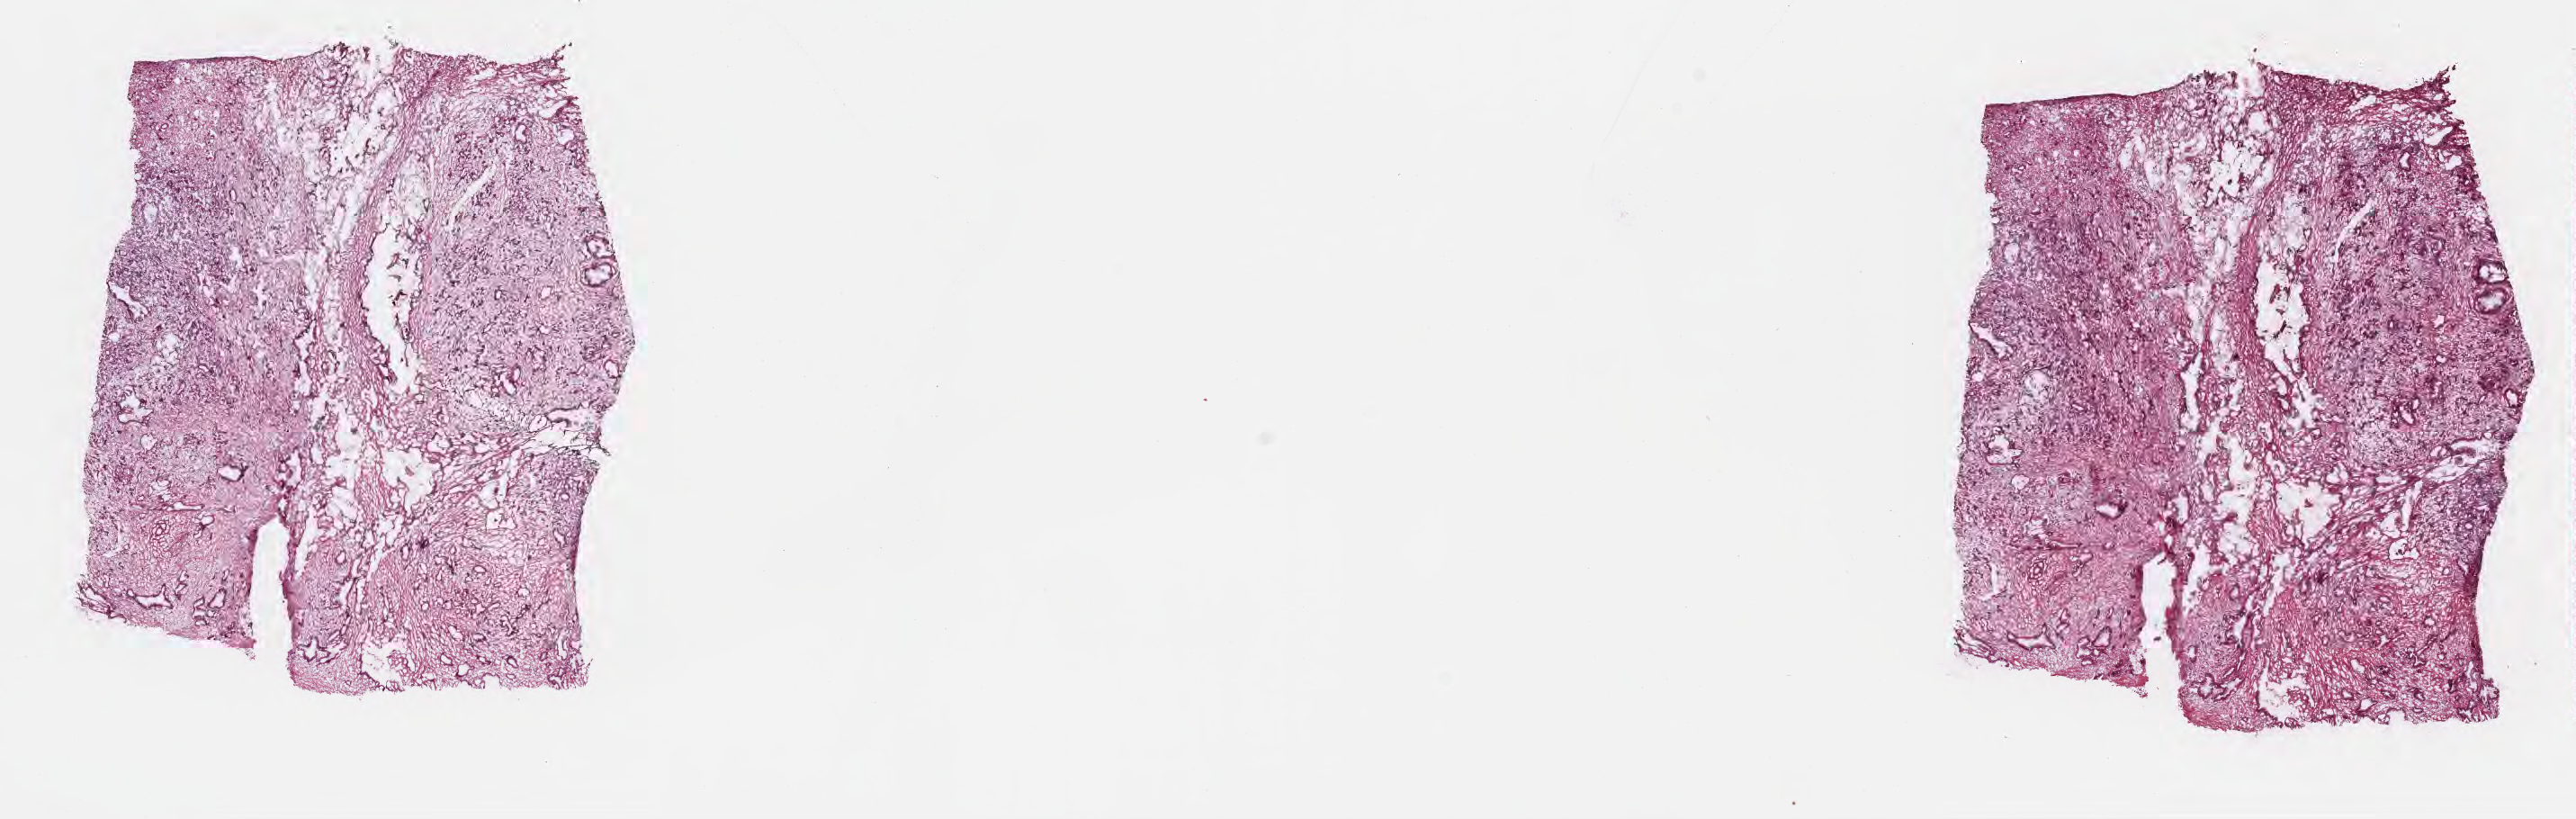
Whole-slide image, hematoxylin and eosin (H&E) stain — a low-resolution overview of the entire scanned area, about 23.2 x 7.4 mm; cryosection; primary tumor; anatomic site: head of pancreas. Male patient; age at initial diagnosis 63 years. Tumor grade: G2 (moderately differentiated). Pathologist review of this section (percent, as recorded): tumor cells 20%, tumor nuclei 40%, stromal cells 60%, necrosis 0%, normal cells 20%. Inflammatory infiltration, as recorded: lymphocyte infiltration 0%, monocyte infiltration 0%, neutrophil infiltration 0%.
Diagnosis: Infiltrating duct carcinoma, NOS. AJCC pathologic stage: Stage III.